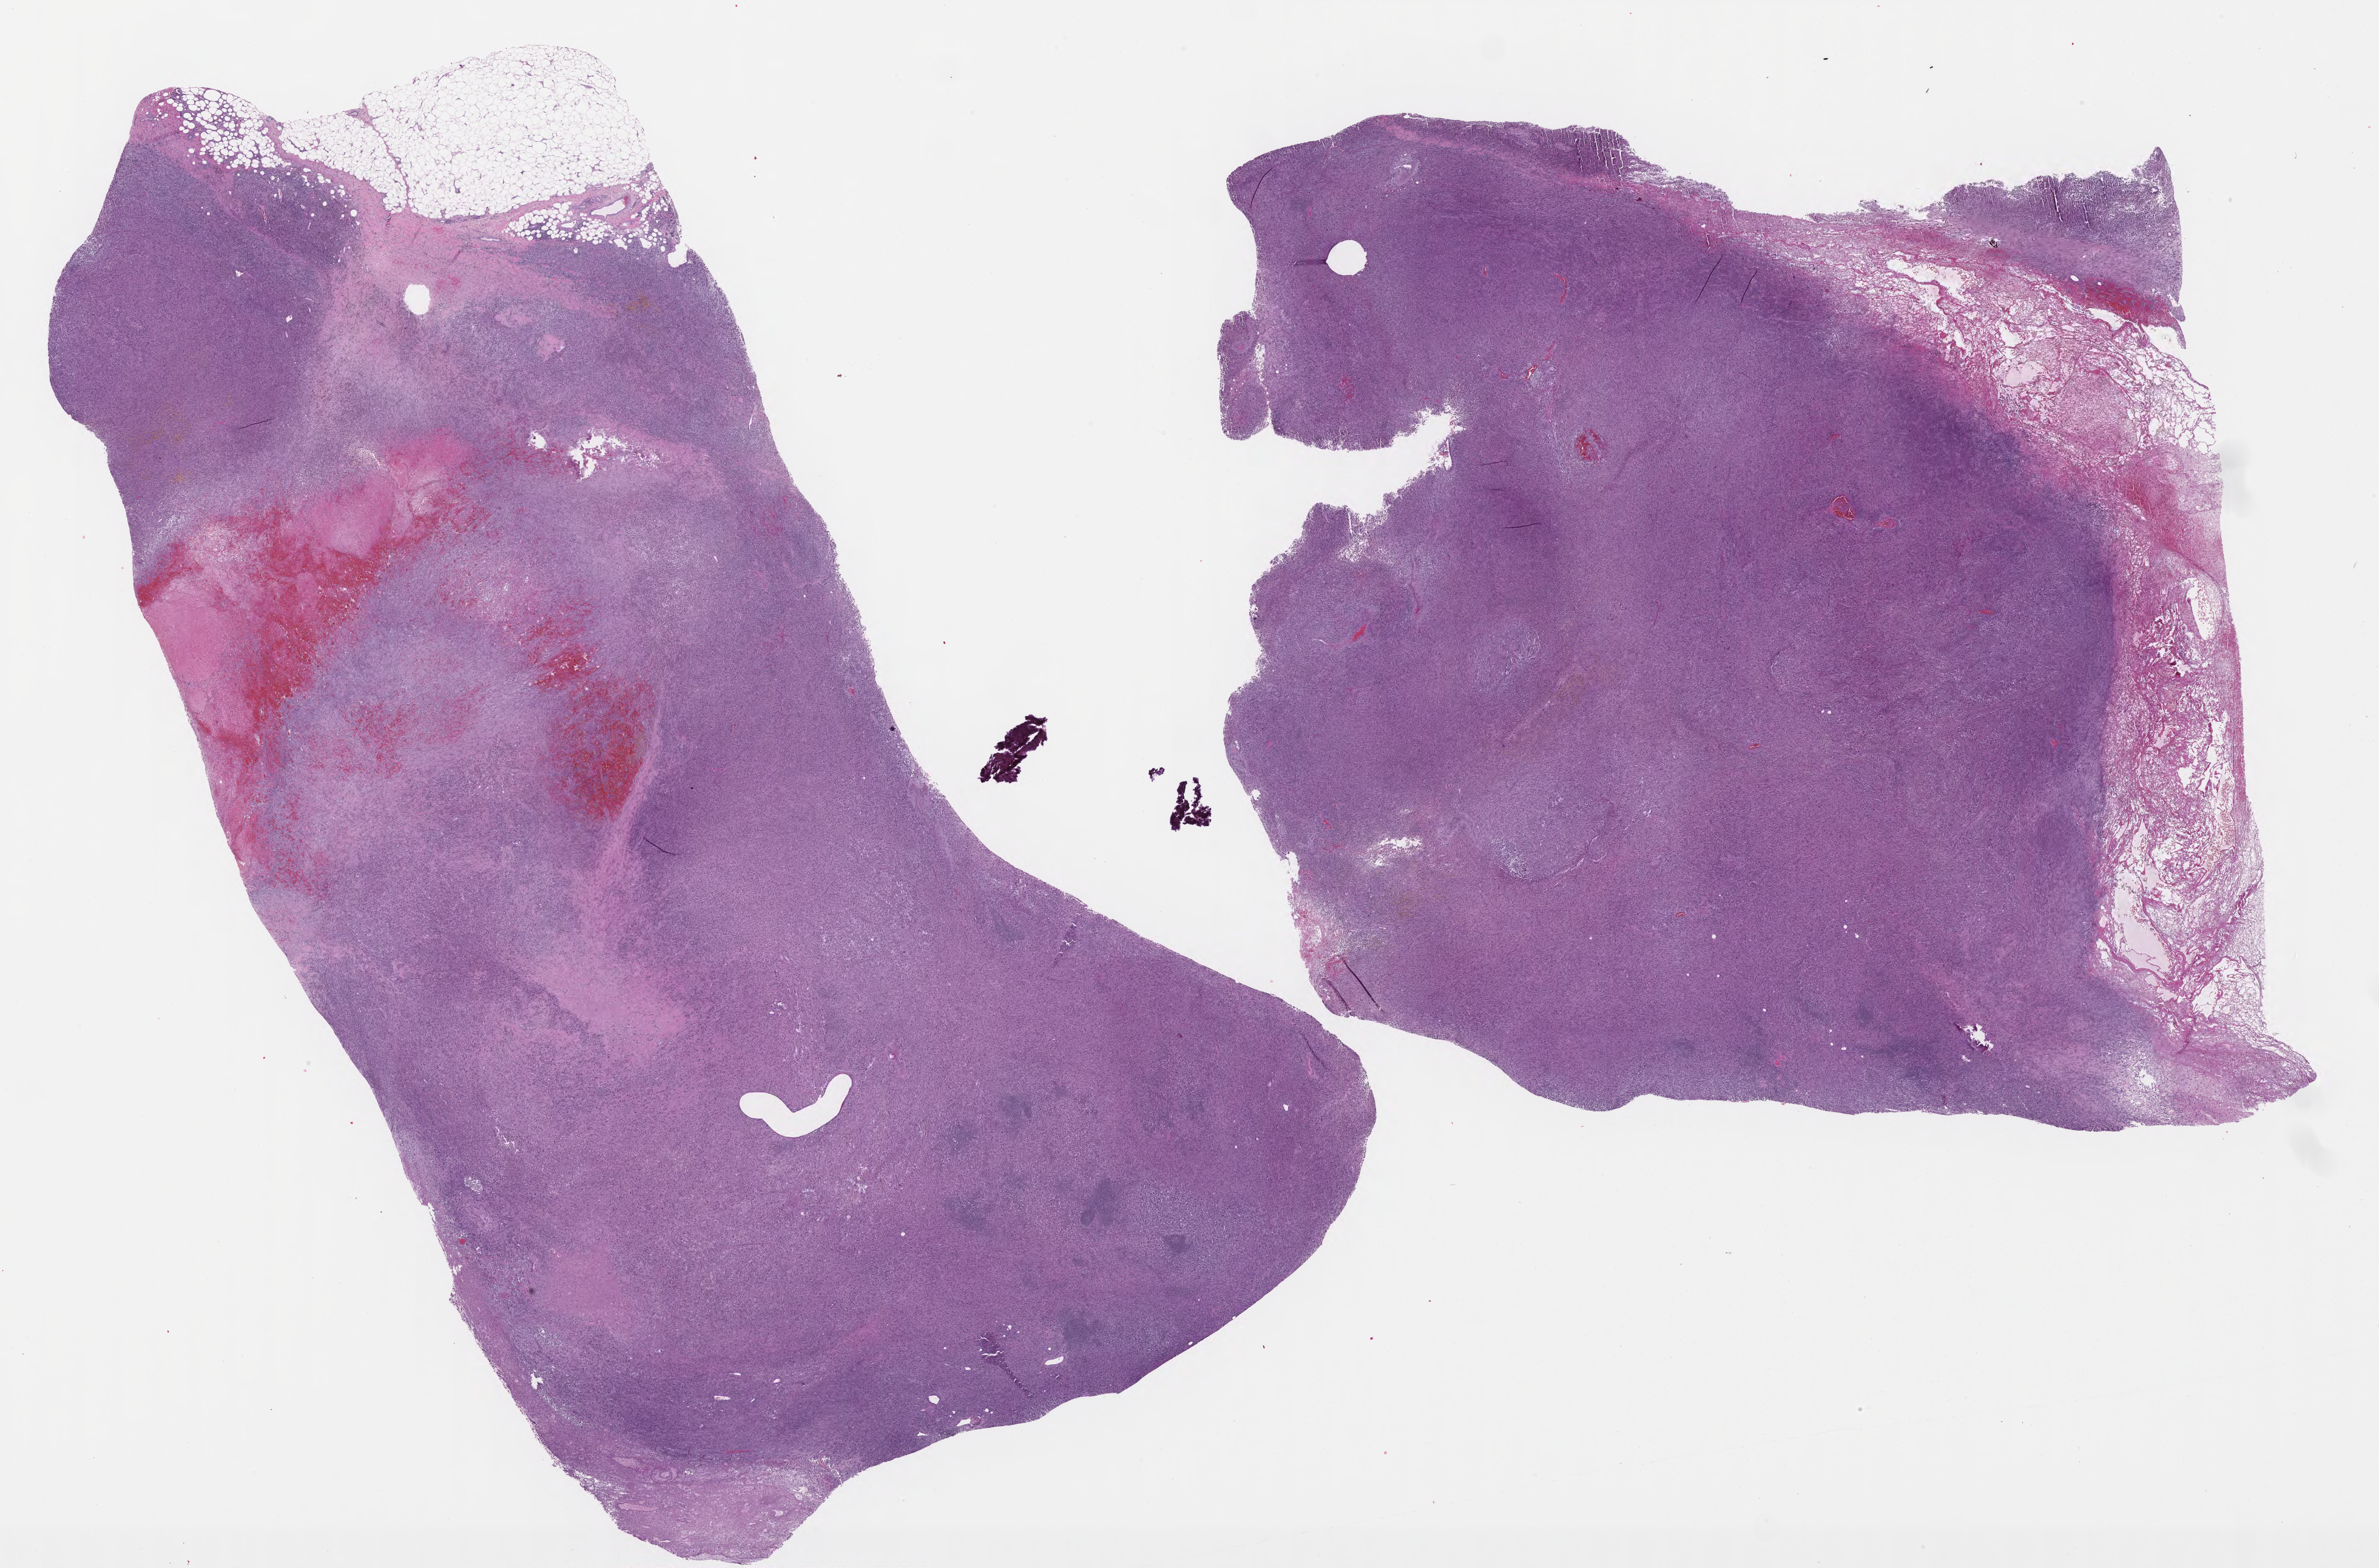
Whole-slide histology image, Hematoxylin and eosin (H&E) stained, a low-resolution overview of the entire scanned area, about 31.5 x 20.8 mm (acquisition: 40x scan), formalin-fixed paraffin-embedded (FFPE) diagnostic section, connective, subcutaneous and other soft tissues, primary tumour sample. Male patient; age at initial diagnosis 63 years.
Histologic diagnosis: Malignant fibrous histiocytoma.